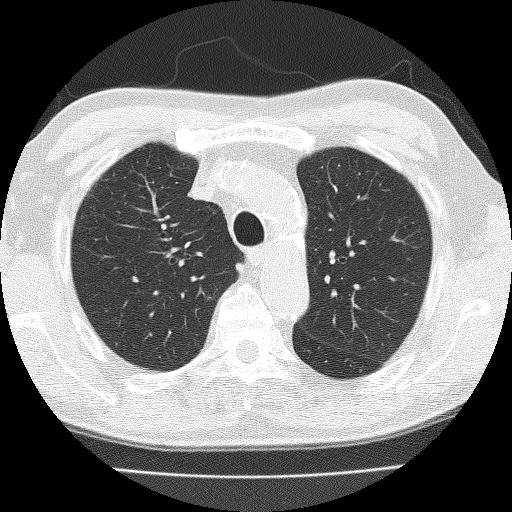
Chest CT (low-dose screening protocol), one axial image; second annual screen; lung window (W 1500 / L -600 HU); 2 mm slice thickness; lung (sharp) reconstruction kernel (FC51); 512 × 512 image matrix. Male, age 72 years at enrolment. Current smoker at enrolment.
Expert-annotated lung lesion, box from (x=190, y=279) to (x=226, y=316) px. Screening reader's record for this exam: no non-calcified nodule ≥4 mm recorded. Participant outcome: lung cancer diagnosed 396 days after this screen — squamous cell carcinoma, NOS, right upper lobe, moderately differentiated (G2), stage IIA (AJCC 6th edition), 25 mm at pathology.